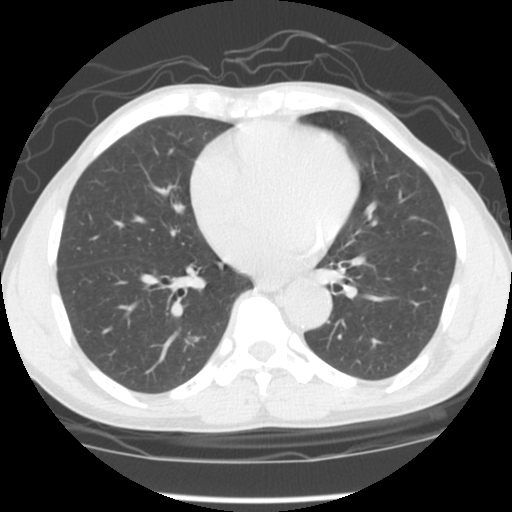
Low-dose screening chest CT, axial slice. Second annual screen. Lung window (W 1500 / L -600 HU). 2.5 mm slice thickness. Slice 47 of 118 in the series. Male participant, aged 58 years at enrolment. Current smoker at enrolment.
Expert reader's lesion annotation, bounding box <170,326,213,361> (left, top, right, bottom; pixels). Reader record for this screening exam (exam-level; its link to the box is not recorded): non-calcified nodule or mass ≥4 mm, left upper lobe, 10 × 10 mm, poorly defined margins, ground glass attenuation, pre-existing on the prior screen: yes; interval growth: no. Note: the box lies in the patient's right hemithorax on this image, whereas the reader's record names the left lung; they may be different findings. Official screen result: positive, no significant change: stable abnormalities potentially related to lung cancer, unchanged since the prior screening exam.